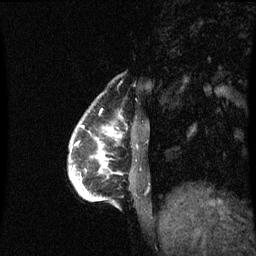
Breast MRI (dynamic contrast-enhanced), one sagittal slice; position 14 of 60 along the scan axis; dynamic contrast-enhanced series, image 2 of 3 at this slice position (ordered by acquisition); 1.5 T; TE 4.2 ms, TR 8.9 ms; 2 mm slice thickness; 256 × 256 image matrix. Patient: female, 35 years. From the clinical record (not read from this slice): setting: breast cancer imaged before/during neoadjuvant chemotherapy; receptor status: HR-positive, HER2-negative.
Annotated regions visible in this slice (semi-automatically segmented with operator editing):
- analysis volume of interest (the breast-tissue region the enhancement analysis was run in; not a lesion): bounding box <69,118,118,207> (left, top, right, bottom; pixels)
- tumour enhancement mask (voxels above the 70 % enhancement threshold inside the analysis volume of interest): <77,146,107,187>